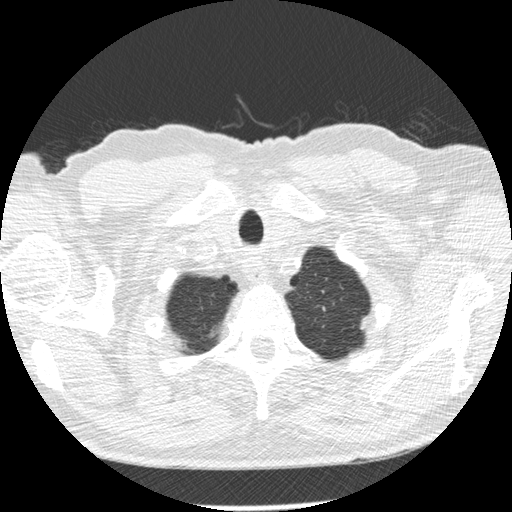
Low-dose screening chest CT, axial slice, second annual screen, lung window (W 1500 / L -600 HU), slice 22 of 276 in the series. Male participant, aged 73 years at enrolment. Former smoker at enrolment.
• Expert-annotated lung lesion, box from (x=347, y=305) to (x=387, y=346) px.
• Screening reader's record for this exam: no non-calcified nodule ≥4 mm recorded.
• Official screen result: negative screen, minor abnormalities not suspicious for lung cancer.
• Lung cancer was diagnosed 457 days after this screen: adenocarcinoma, NOS, left upper lobe, poorly differentiated (G3), stage IB (AJCC 6th edition), 10 mm at pathology.